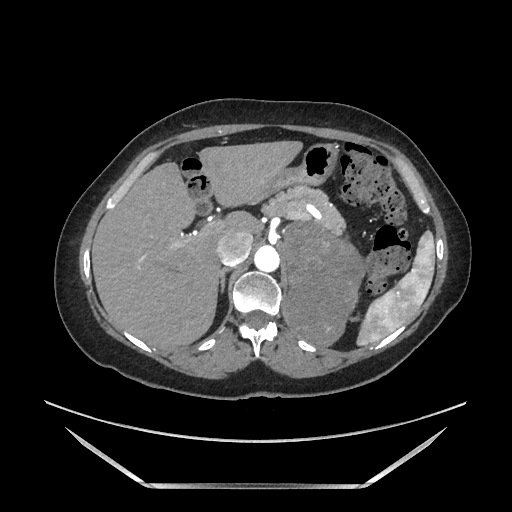
Contrast-enhanced abdominal CT, one axial slice. Position 123 of 205 along the scan axis. Soft-tissue window (W 400 / L 40 HU). 512 × 512 image matrix, field of view 440 × 440 mm. Female patient. Case-level facts recorded for this patient, not image findings: diagnosis: adrenocortical carcinoma; tumour side: left adrenal; tumour size at pathology: 12.5 cm; Ki-67 index: 39 %; stage (as recorded): 3.
Outlined on this slice (semi-automatically segmented with operator editing):
- mass: box from (x=286, y=223) to (x=363, y=343) px